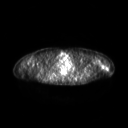
FDG PET of an extremity soft-tissue mass (from a PET/CT study), one axial slice. Slice 200 of 267 in the series (ordered by position). 3.27 mm slice thickness. 128 × 128 image matrix. Patient: female, 28 years. From the clinical record (not read from this slice): histological type: malignant fibrous histiocytoma; grade: low; site of the primary tumour: left arm.
Annotated regions visible in this slice (expert contour drawn on MRI and transferred to this co-registered scan by the dataset authors):
- gross tumour volume (mass): bounding box (x1, y1, x2, y2) in pixels: (101, 64, 106, 69)